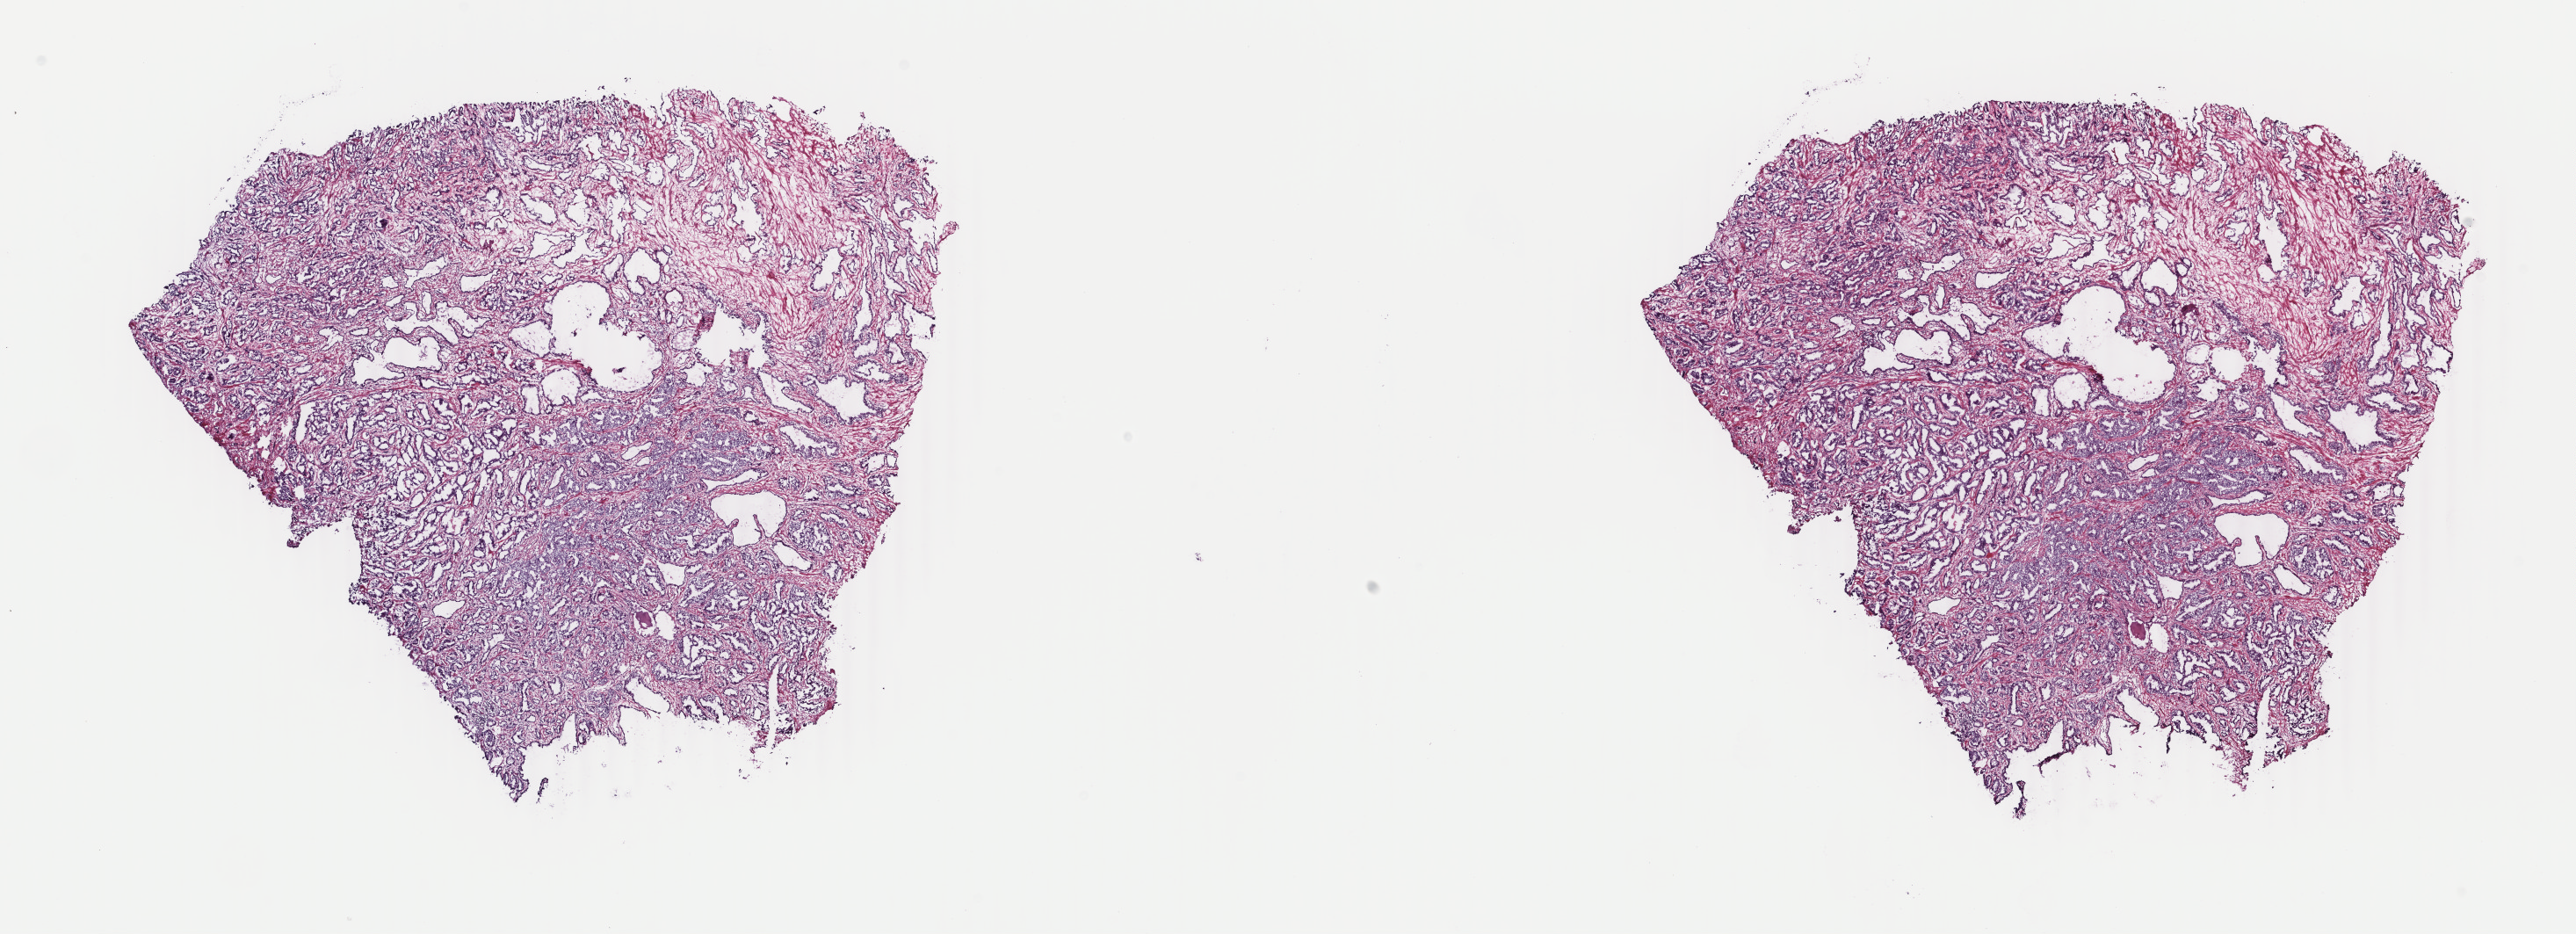
H&E-stained whole-slide image — shown as a low-resolution overview of the whole scanned area (about 23.3 x 8.5 mm, from a 40x scan). Frozen section from the top of the tissue portion. Primary tumour sample from the prostate. Male, age 76 years at initial diagnosis. Gleason score: 9 (4+5). Composition of this section per pathologist review: tumour cells 60%, tumour nuclei 70%, normal cells 40%, stromal cells 0%, necrosis 0%. Infiltration values recorded for this section: lymphocyte infiltration 0%, monocyte infiltration 0%, neutrophil infiltration 0%.
* laterality: bilateral
* pathologic diagnosis: Adenocarcinoma, NOS